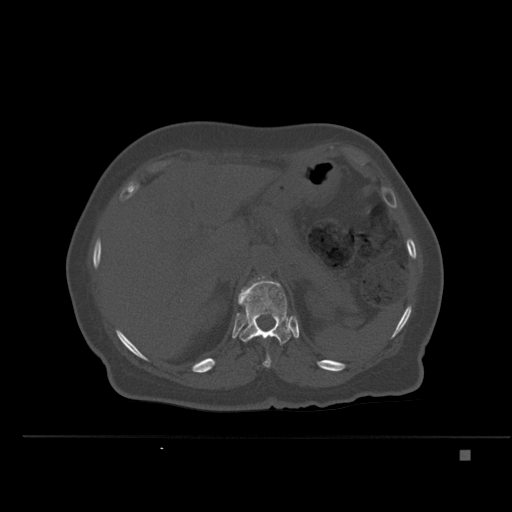
CT including the spine, one axial slice. Position 255 of 477 along the scan axis. Bone window (W 1800 / L 400 HU). 1.5 mm slice thickness. 512 × 512 image matrix, field of view 422 × 422 mm. Patient: female, 74 years. Case-level facts recorded for this patient, not image findings: primary cancer: colon.
Outlined on this slice (semi-automatically segmented with operator editing):
- L1 vertebra: bounding box <258,276,265,279> (left, top, right, bottom; pixels)
- T11 vertebra: <254,336,271,368>
- T12 vertebra: <238,280,292,345>